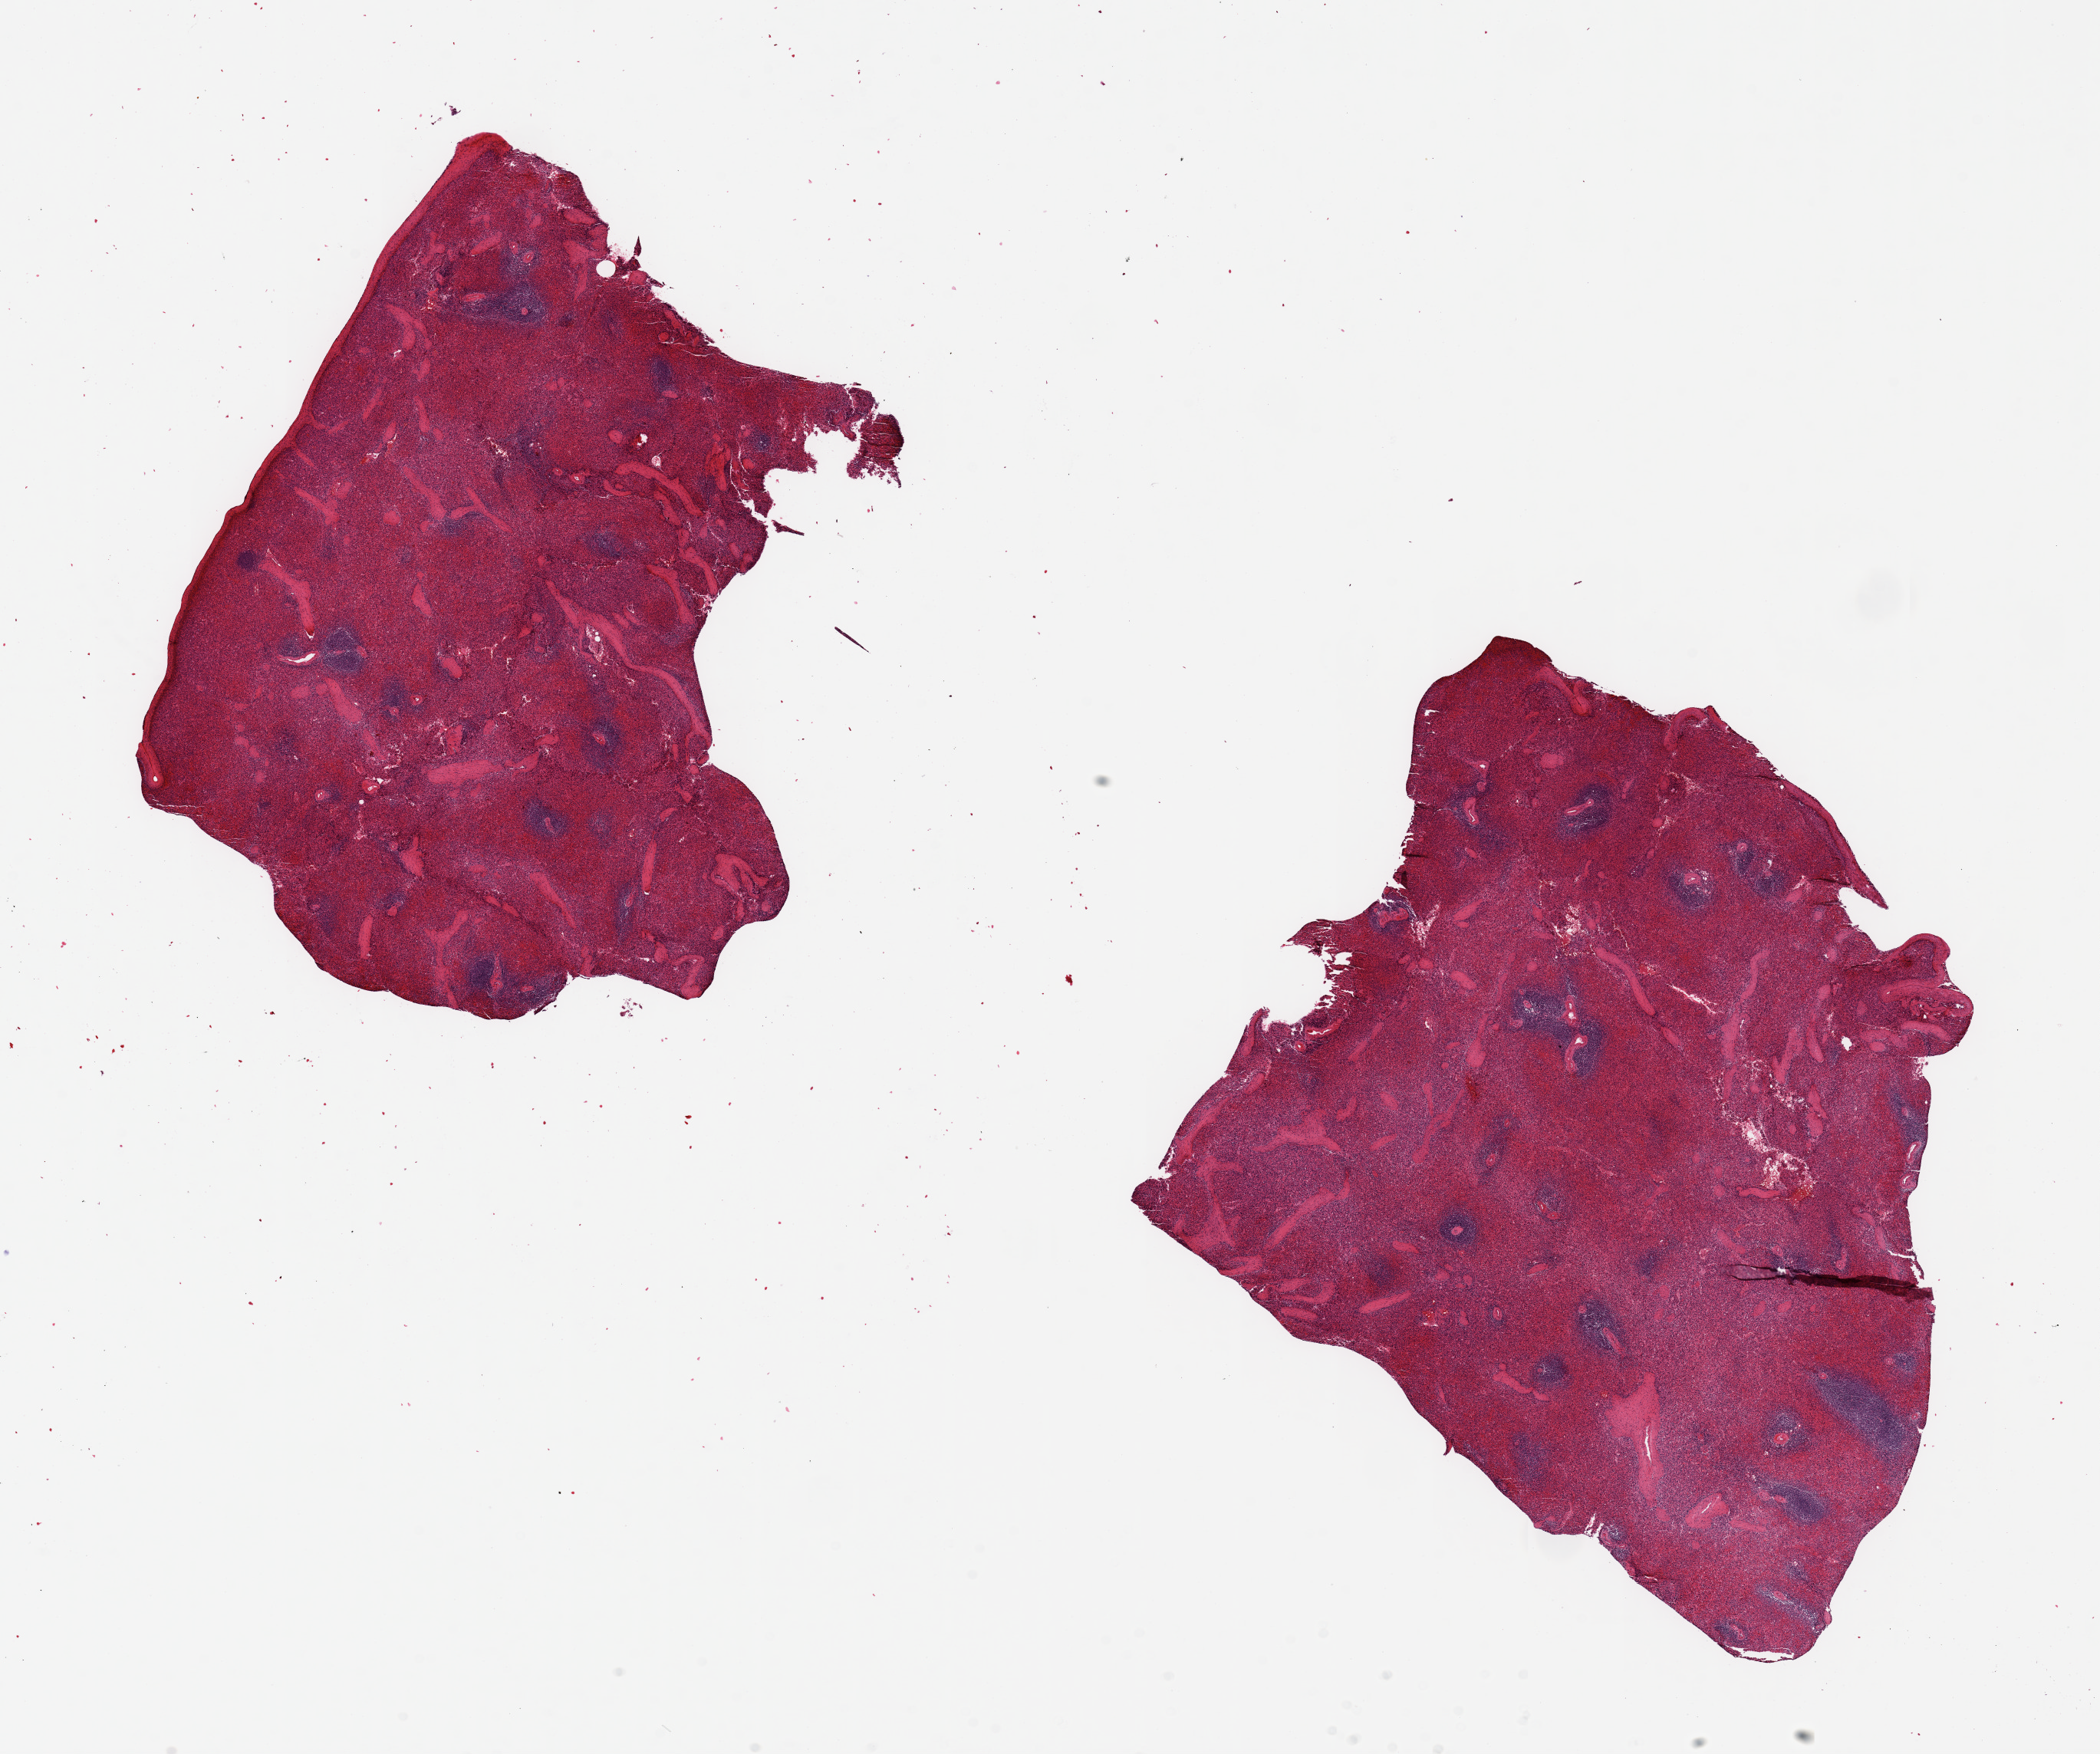
Whole-slide image, haematoxylin and eosin stain — whole scanned area (about 21.7 x 18.1 mm, from a 20x scan) shown as a low-resolution overview; PAXgene-fixed, paraffin-embedded tissue; sampled site (target tissue): spleen; donor tissue sample. Male donor.
Reviewer comment on this tissue sample: 2 pieces ~ 6x5mm. Moderate congestion, poorly preserved.